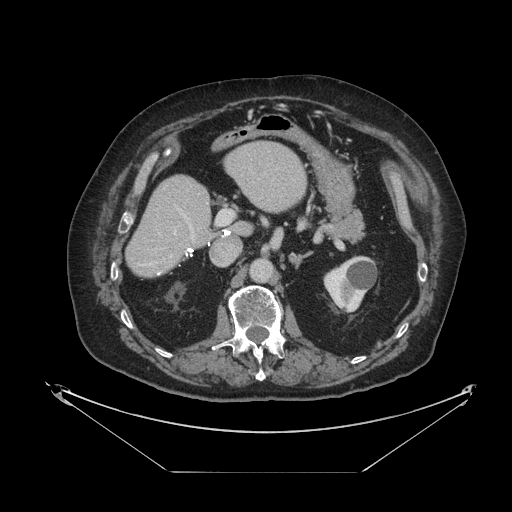
Contrast-enhanced abdominal CT, one axial slice; slice 51 of 121 in the series (ordered by position); reconstruction kernel STANDARD; intravenous contrast given; soft-tissue window (W 400 / L 40 HU); 2.5 mm slice thickness; 512 × 512 image matrix, field of view 500 × 500 mm. Male patient, age 68 years. Case-level facts recorded for this patient, not image findings: diagnosis: colorectal cancer liver metastases, imaged before liver resection; multiple liver metastases: no; largest metastasis: 4 cm; chemotherapy before resection: yes.
Outlined on this slice (expert manual segmentation):
- hepatic veins: bounding box (x1, y1, x2, y2) in pixels: (169, 256, 172, 264)
- liver: (128, 143, 306, 276)
- planned liver remnant (the part of the liver to remain after resection): (128, 142, 306, 276)
- portal vein (with intrahepatic branches): (178, 208, 233, 242)